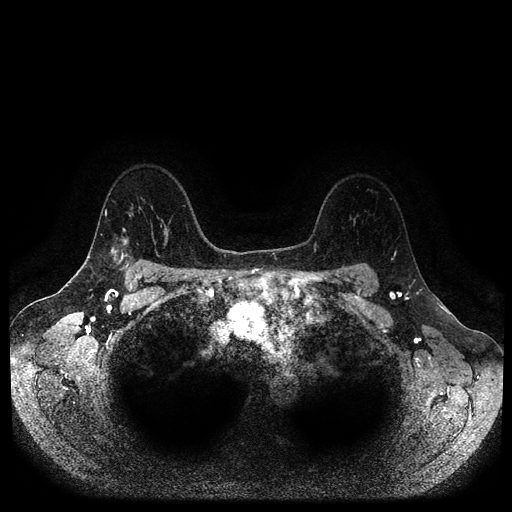
Breast MRI (dynamic contrast-enhanced, multi-phase), one axial slice. Slice 76 of 116 in the series (ordered by position). Dynamic contrast-enhanced series, time point 2 of 5 at this slice position (early post-contrast). 1.5 T. TE 2.6 ms, TR 5.3 ms. 512 × 512 image matrix, field of view 360 × 360 mm. Patient: female, 45 years.
Structures marked on this image (semi-automatic segmentation, software-assisted and operator-edited):
- breast lesion (labelled 'tumour' in the annotation; benign lesions carry a separate 'benign' label): bounding box (x1, y1, x2, y2) in pixels: (110, 246, 131, 269)